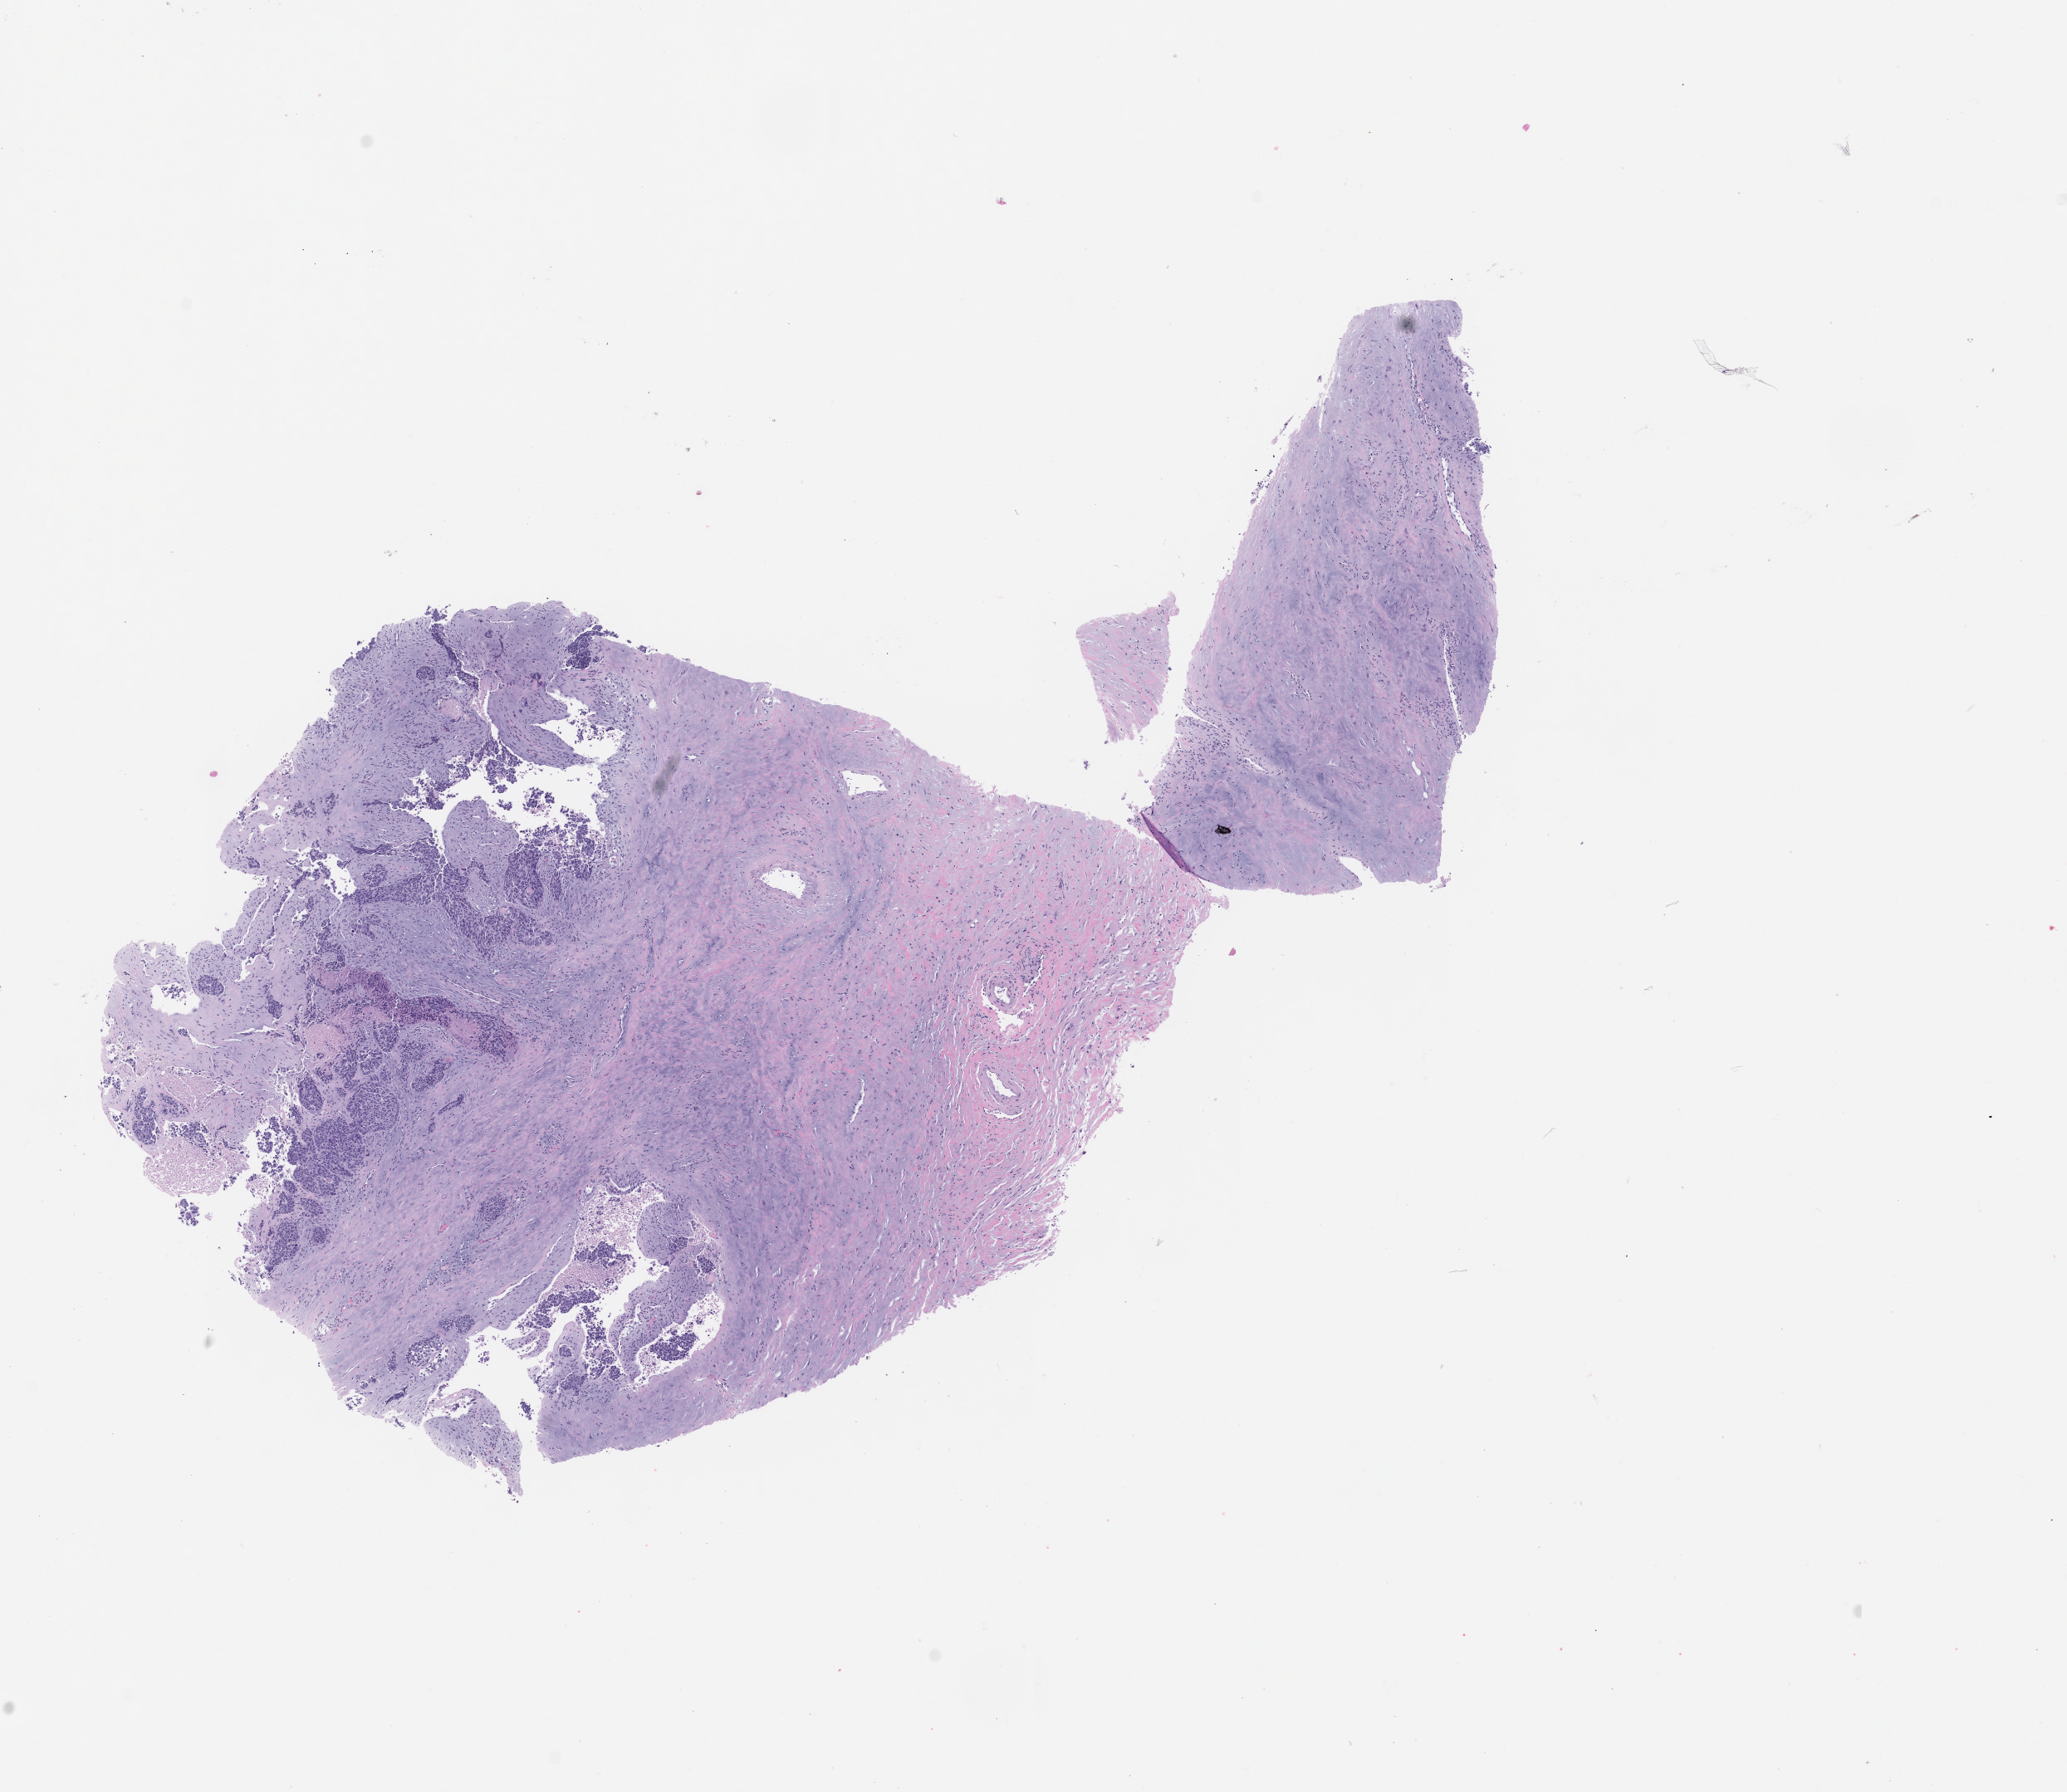
Whole-slide image, hematoxylin and eosin (H&E) stain of the patient's (originator) tumor tissue — whole scanned area (about 10.0 x 8.6 mm) shown as a low-resolution overview. Formalin-fixed, paraffin-embedded (FFPE) tissue. Originating tumor site category: lung. Patient: female, age 66 years.
• diagnosis: Lung Squamous Cell Carcinoma